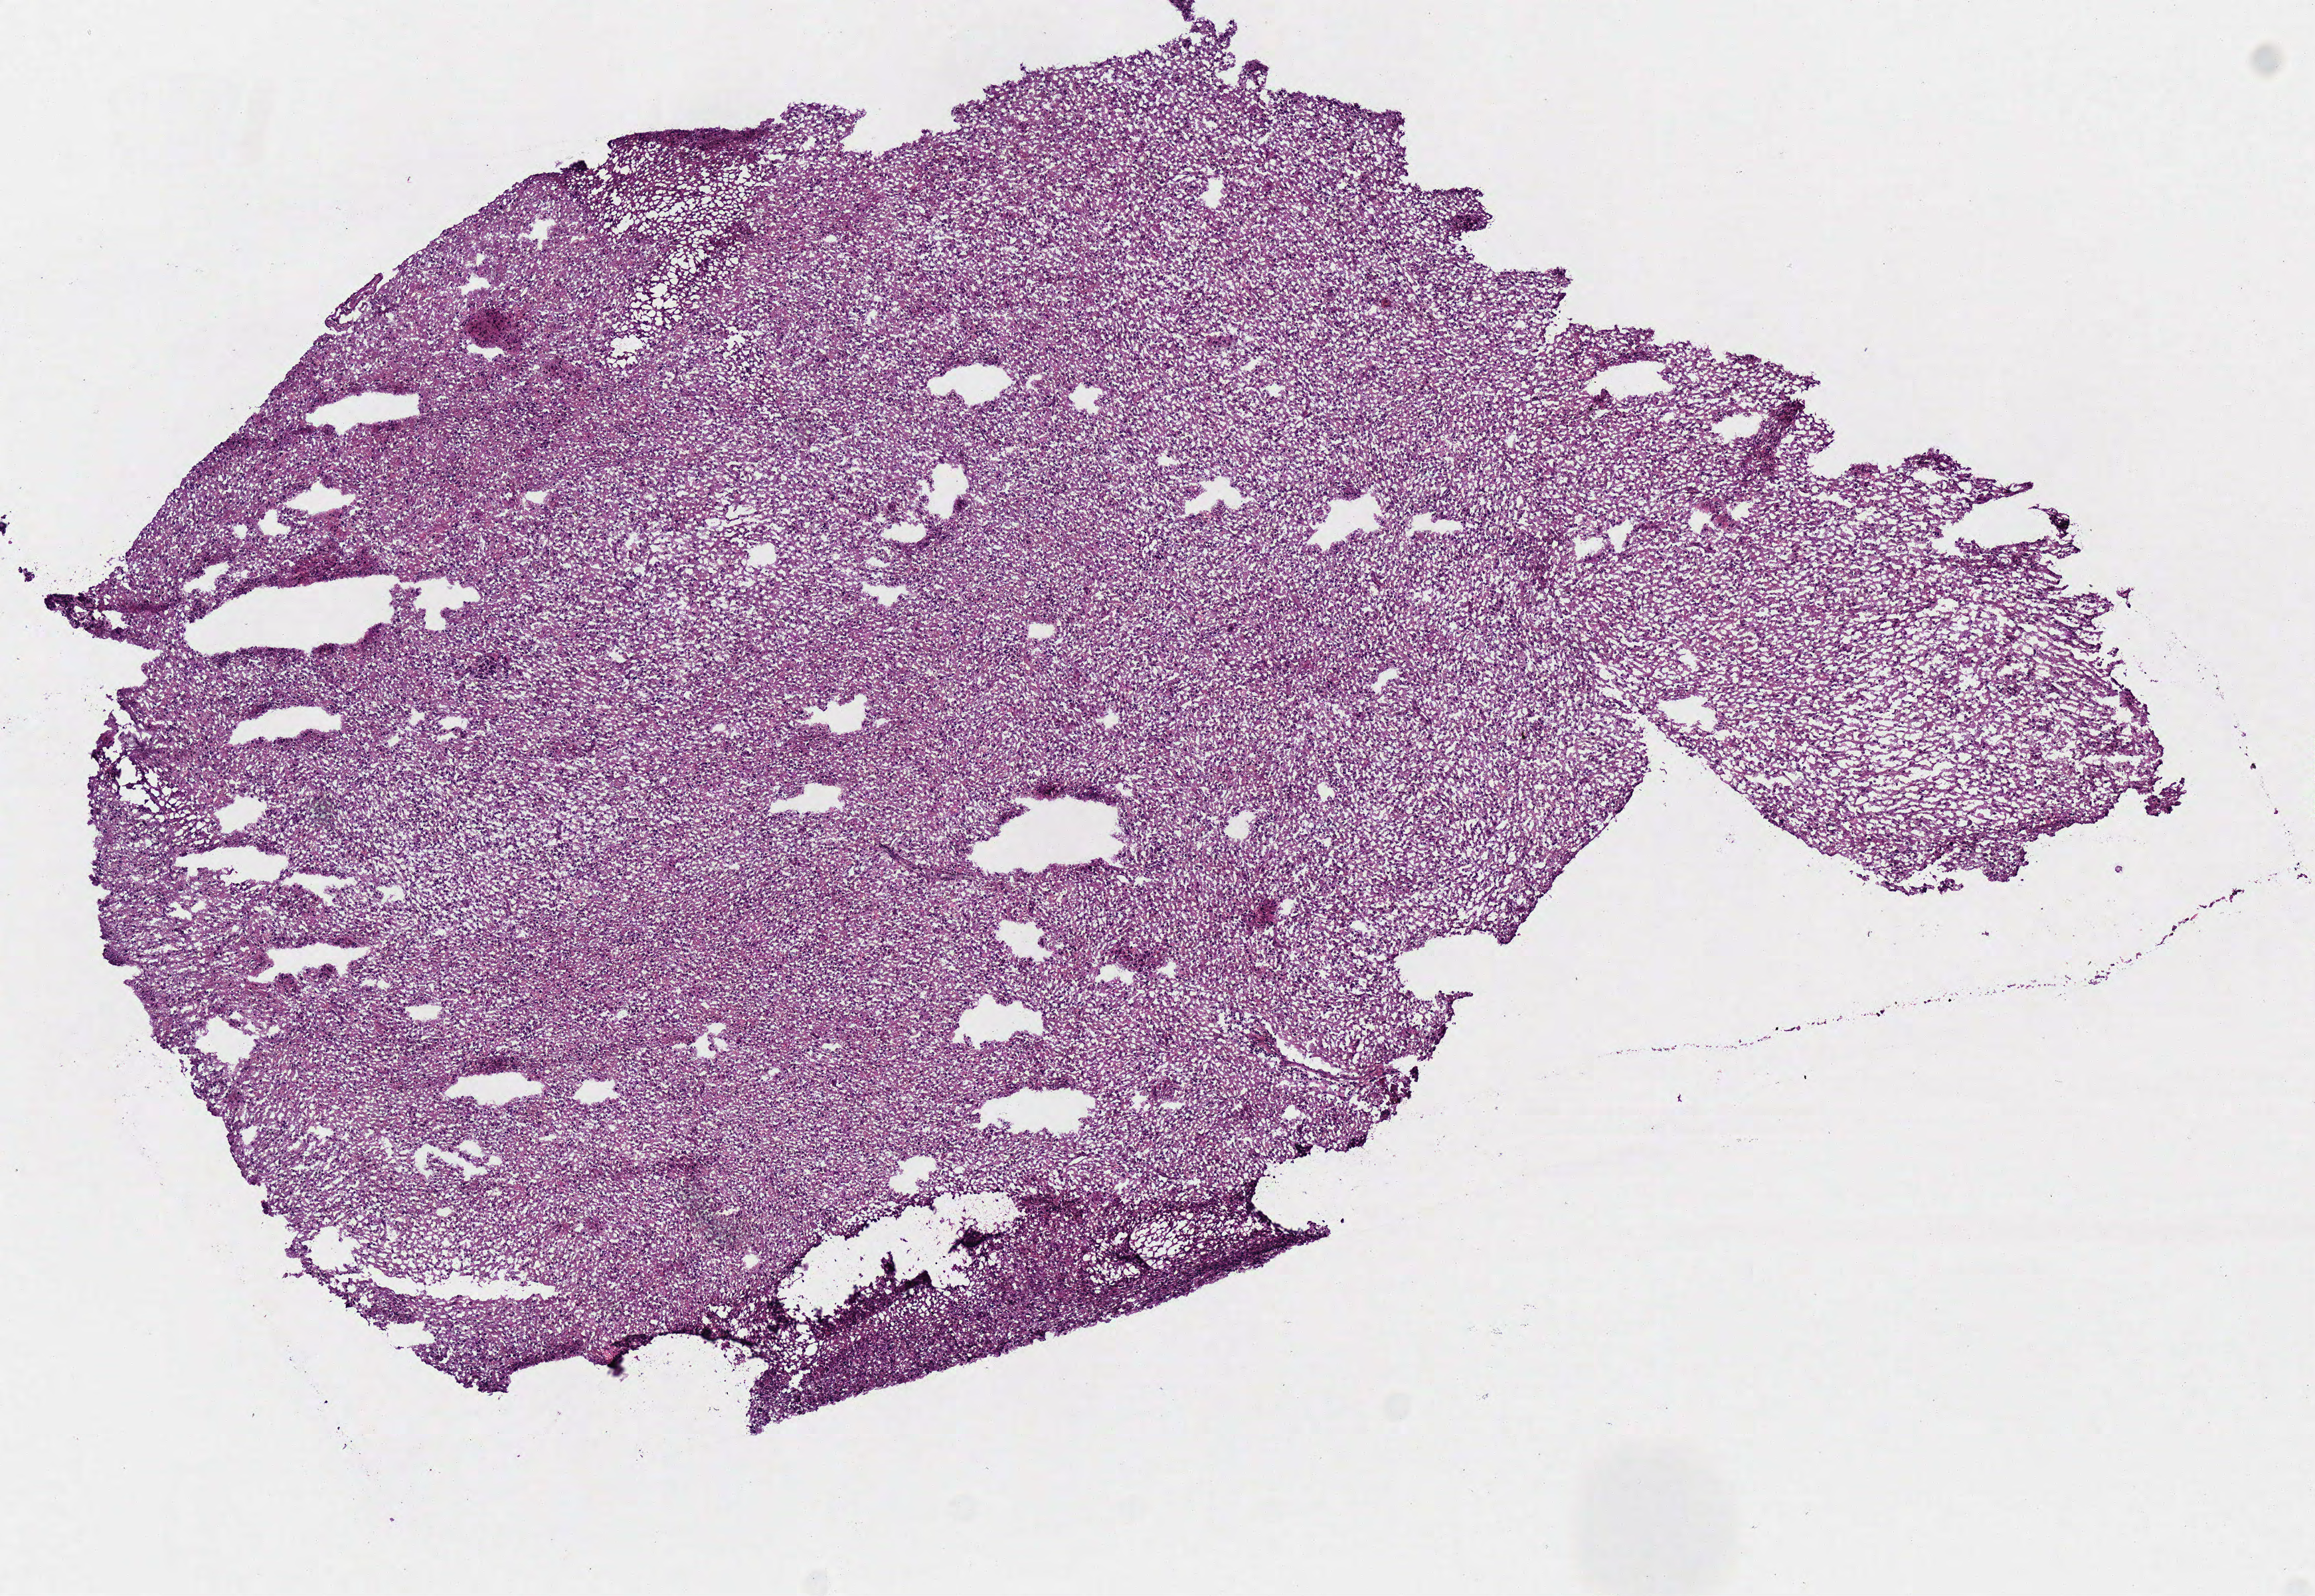
Whole-slide histology image, H&E-stained — whole scanned area (about 6.9 x 4.7 mm, from a 40x scan) shown as a low-resolution overview. Frozen section from the top of the tissue portion. Sample: primary tumour, brain. Male, age 60 years at initial diagnosis. Pathologist review of this section (percent, as recorded): tumour cells 100%, tumour nuclei 75%, normal cells 0%, stromal cells 0%, necrosis 0%.
* diagnosis: Glioblastoma